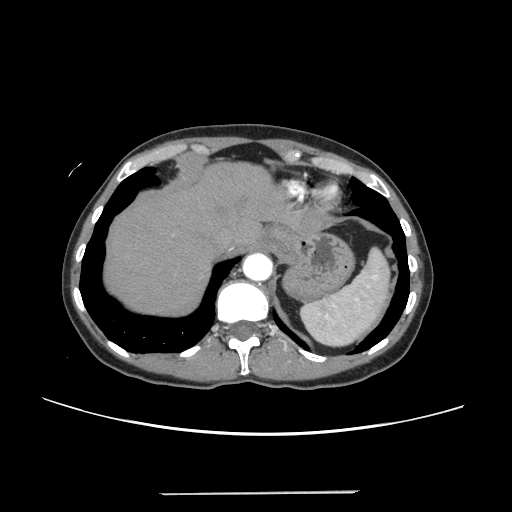
Contrast-enhanced abdominal CT, one axial slice; slice 206 of 240 in the series (ordered by position); intravenous contrast given; soft-tissue window (W 400 / L 40 HU); 1.25 mm slice thickness; 512 × 512 image matrix, field of view 371 × 371 mm. Female patient, age 60 years. Case-level facts recorded for this patient, not image findings: diagnosis: colorectal cancer liver metastases, imaged before liver resection; multiple liver metastases: no; largest metastasis: 1.5 cm; disease in both lobes: no.
Annotated regions visible in this slice (expert manual segmentation):
- hepatic veins: bounding box (x1, y1, x2, y2) in pixels: (221, 223, 250, 245)
- liver: (105, 163, 307, 314)
- planned liver remnant (the part of the liver to remain after resection): (105, 163, 304, 314)